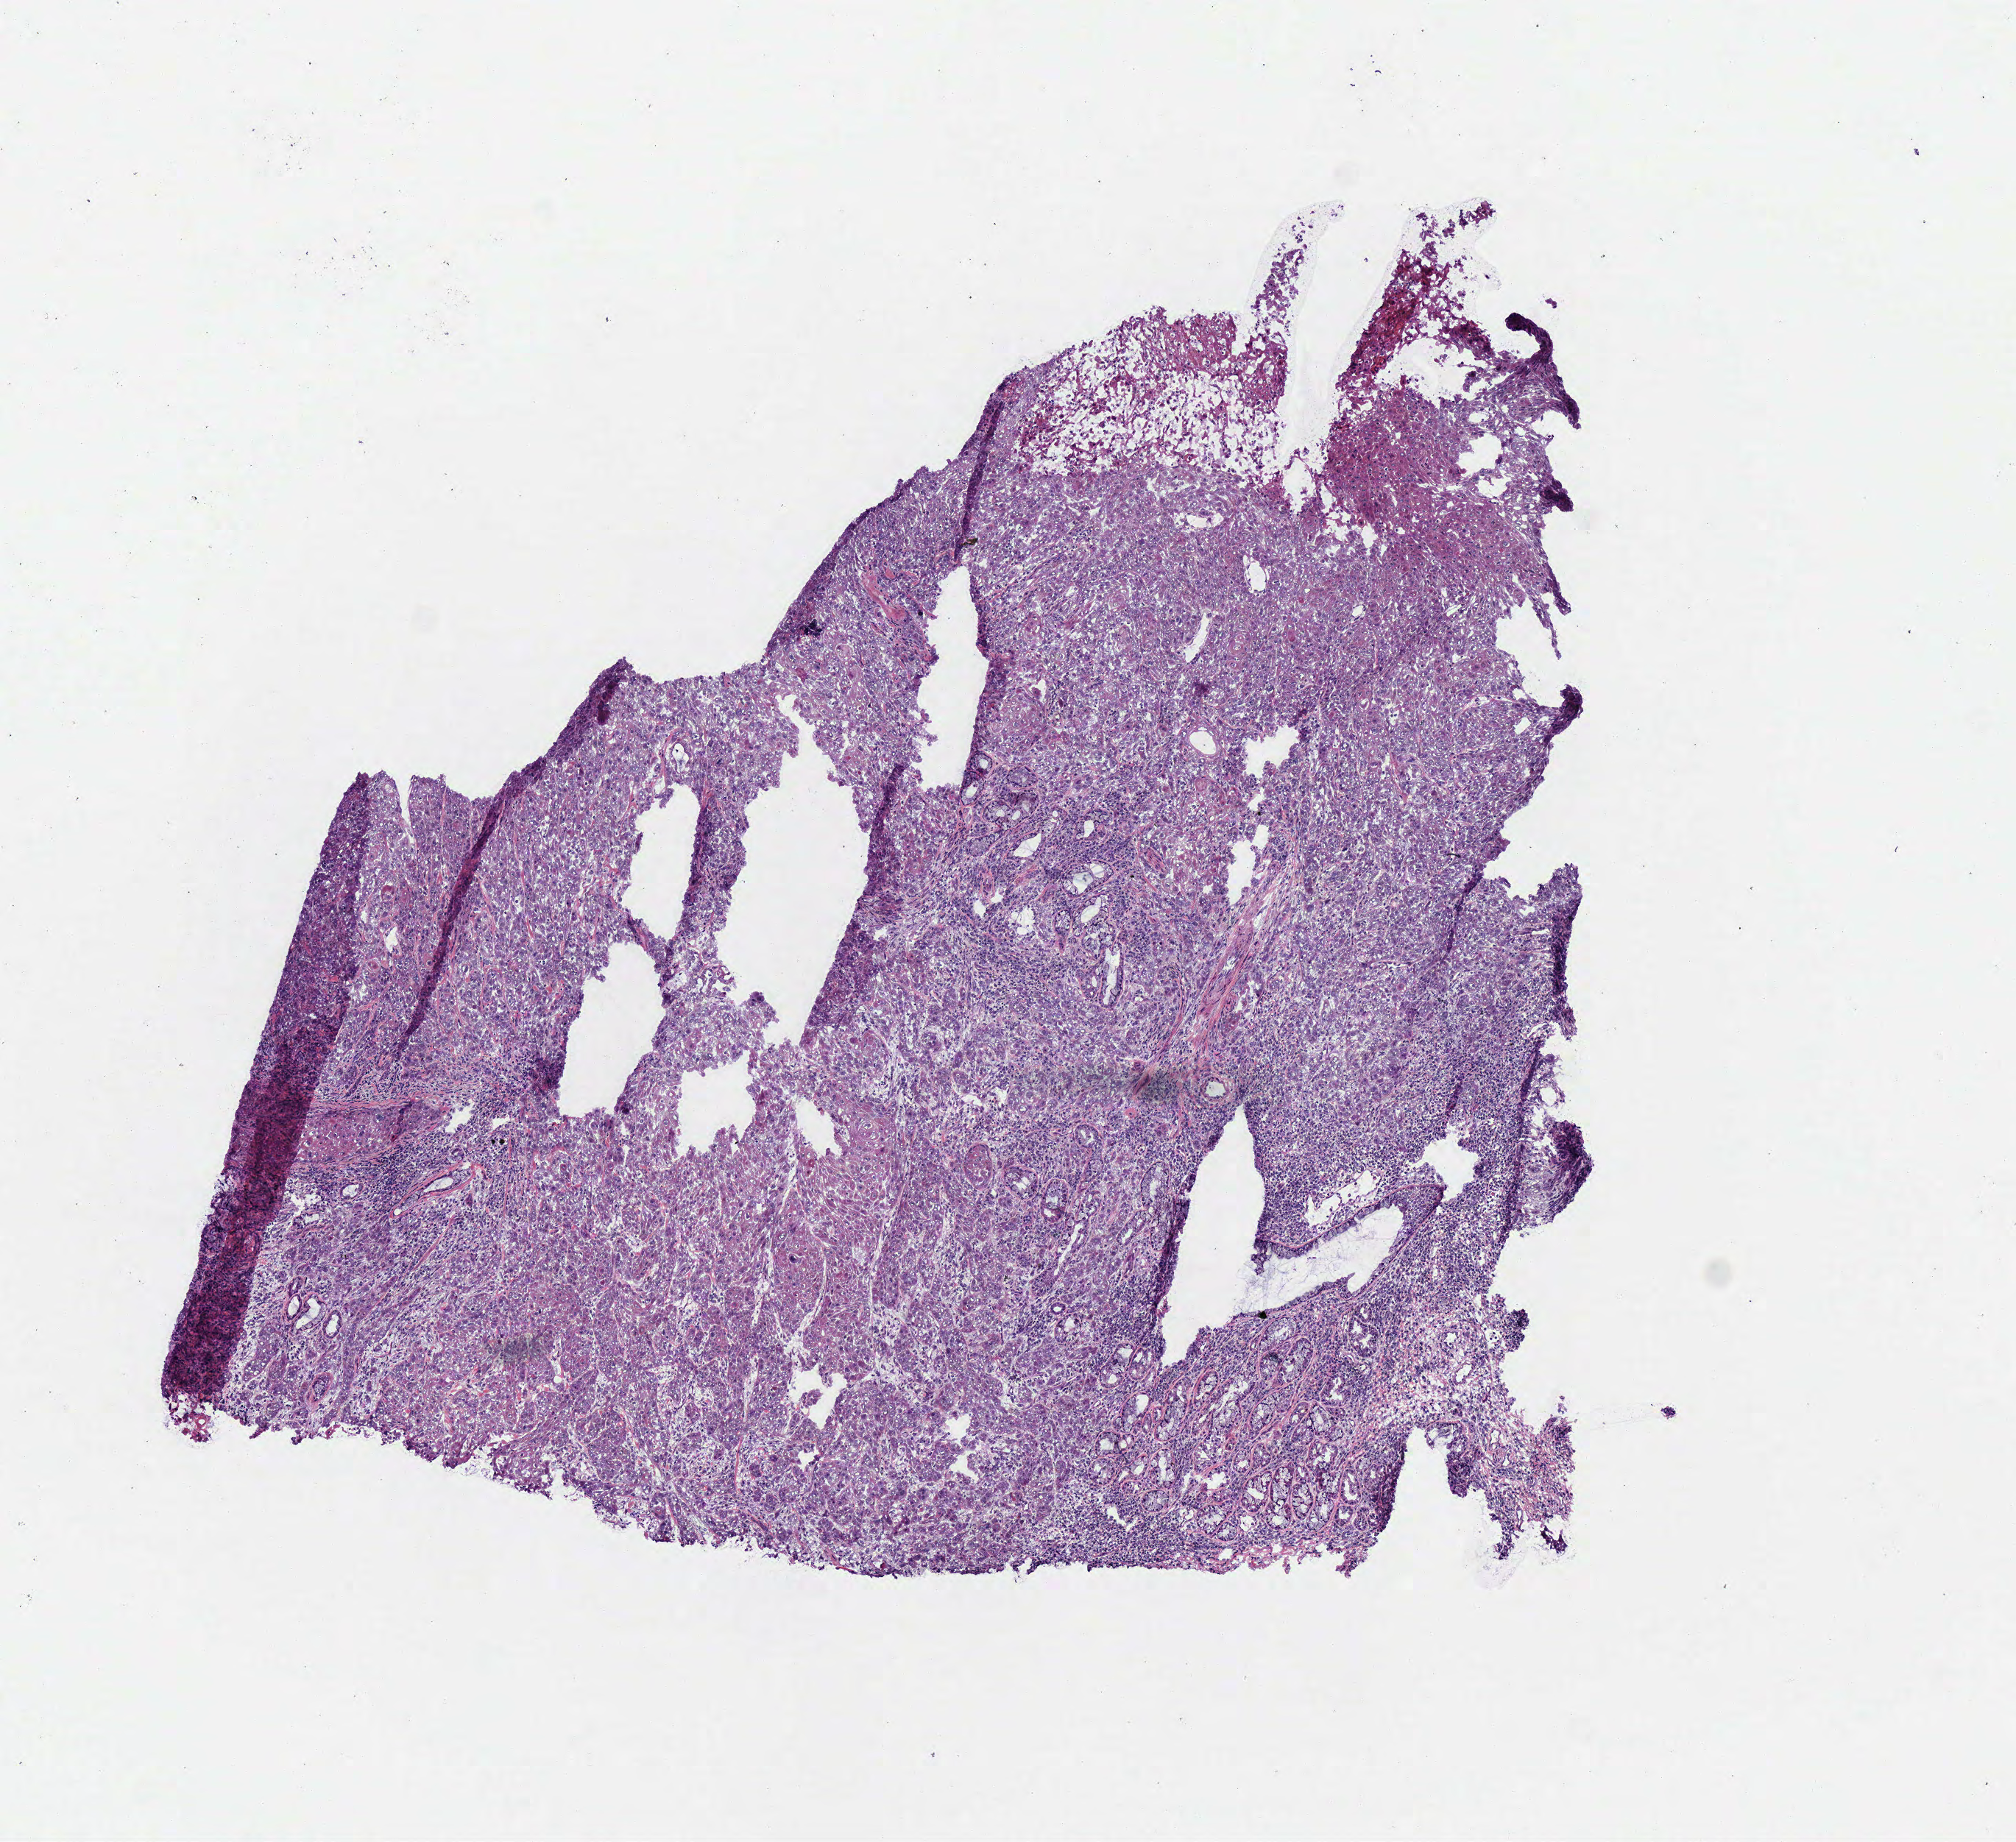
Digitized H&E-stained tissue section (whole slide) — shown as a low-resolution overview of the whole scanned area (about 5.4 x 4.9 mm, slide scanned at 40x), frozen section, primary tumour sample from the head and neck. Male patient; age at initial diagnosis 59 years. Histologic grade: G2 (moderately differentiated). Composition of this section per pathologist review: tumour cells 90%, tumour nuclei 80%, normal cells 0%, stromal cells 10%, necrosis 0%.
AJCC pathologic stage: III (7th edition). Pathologic diagnosis: Squamous cell carcinoma, NOS (larynx, NOS). TNM: T3 N0. Laterality: midline.